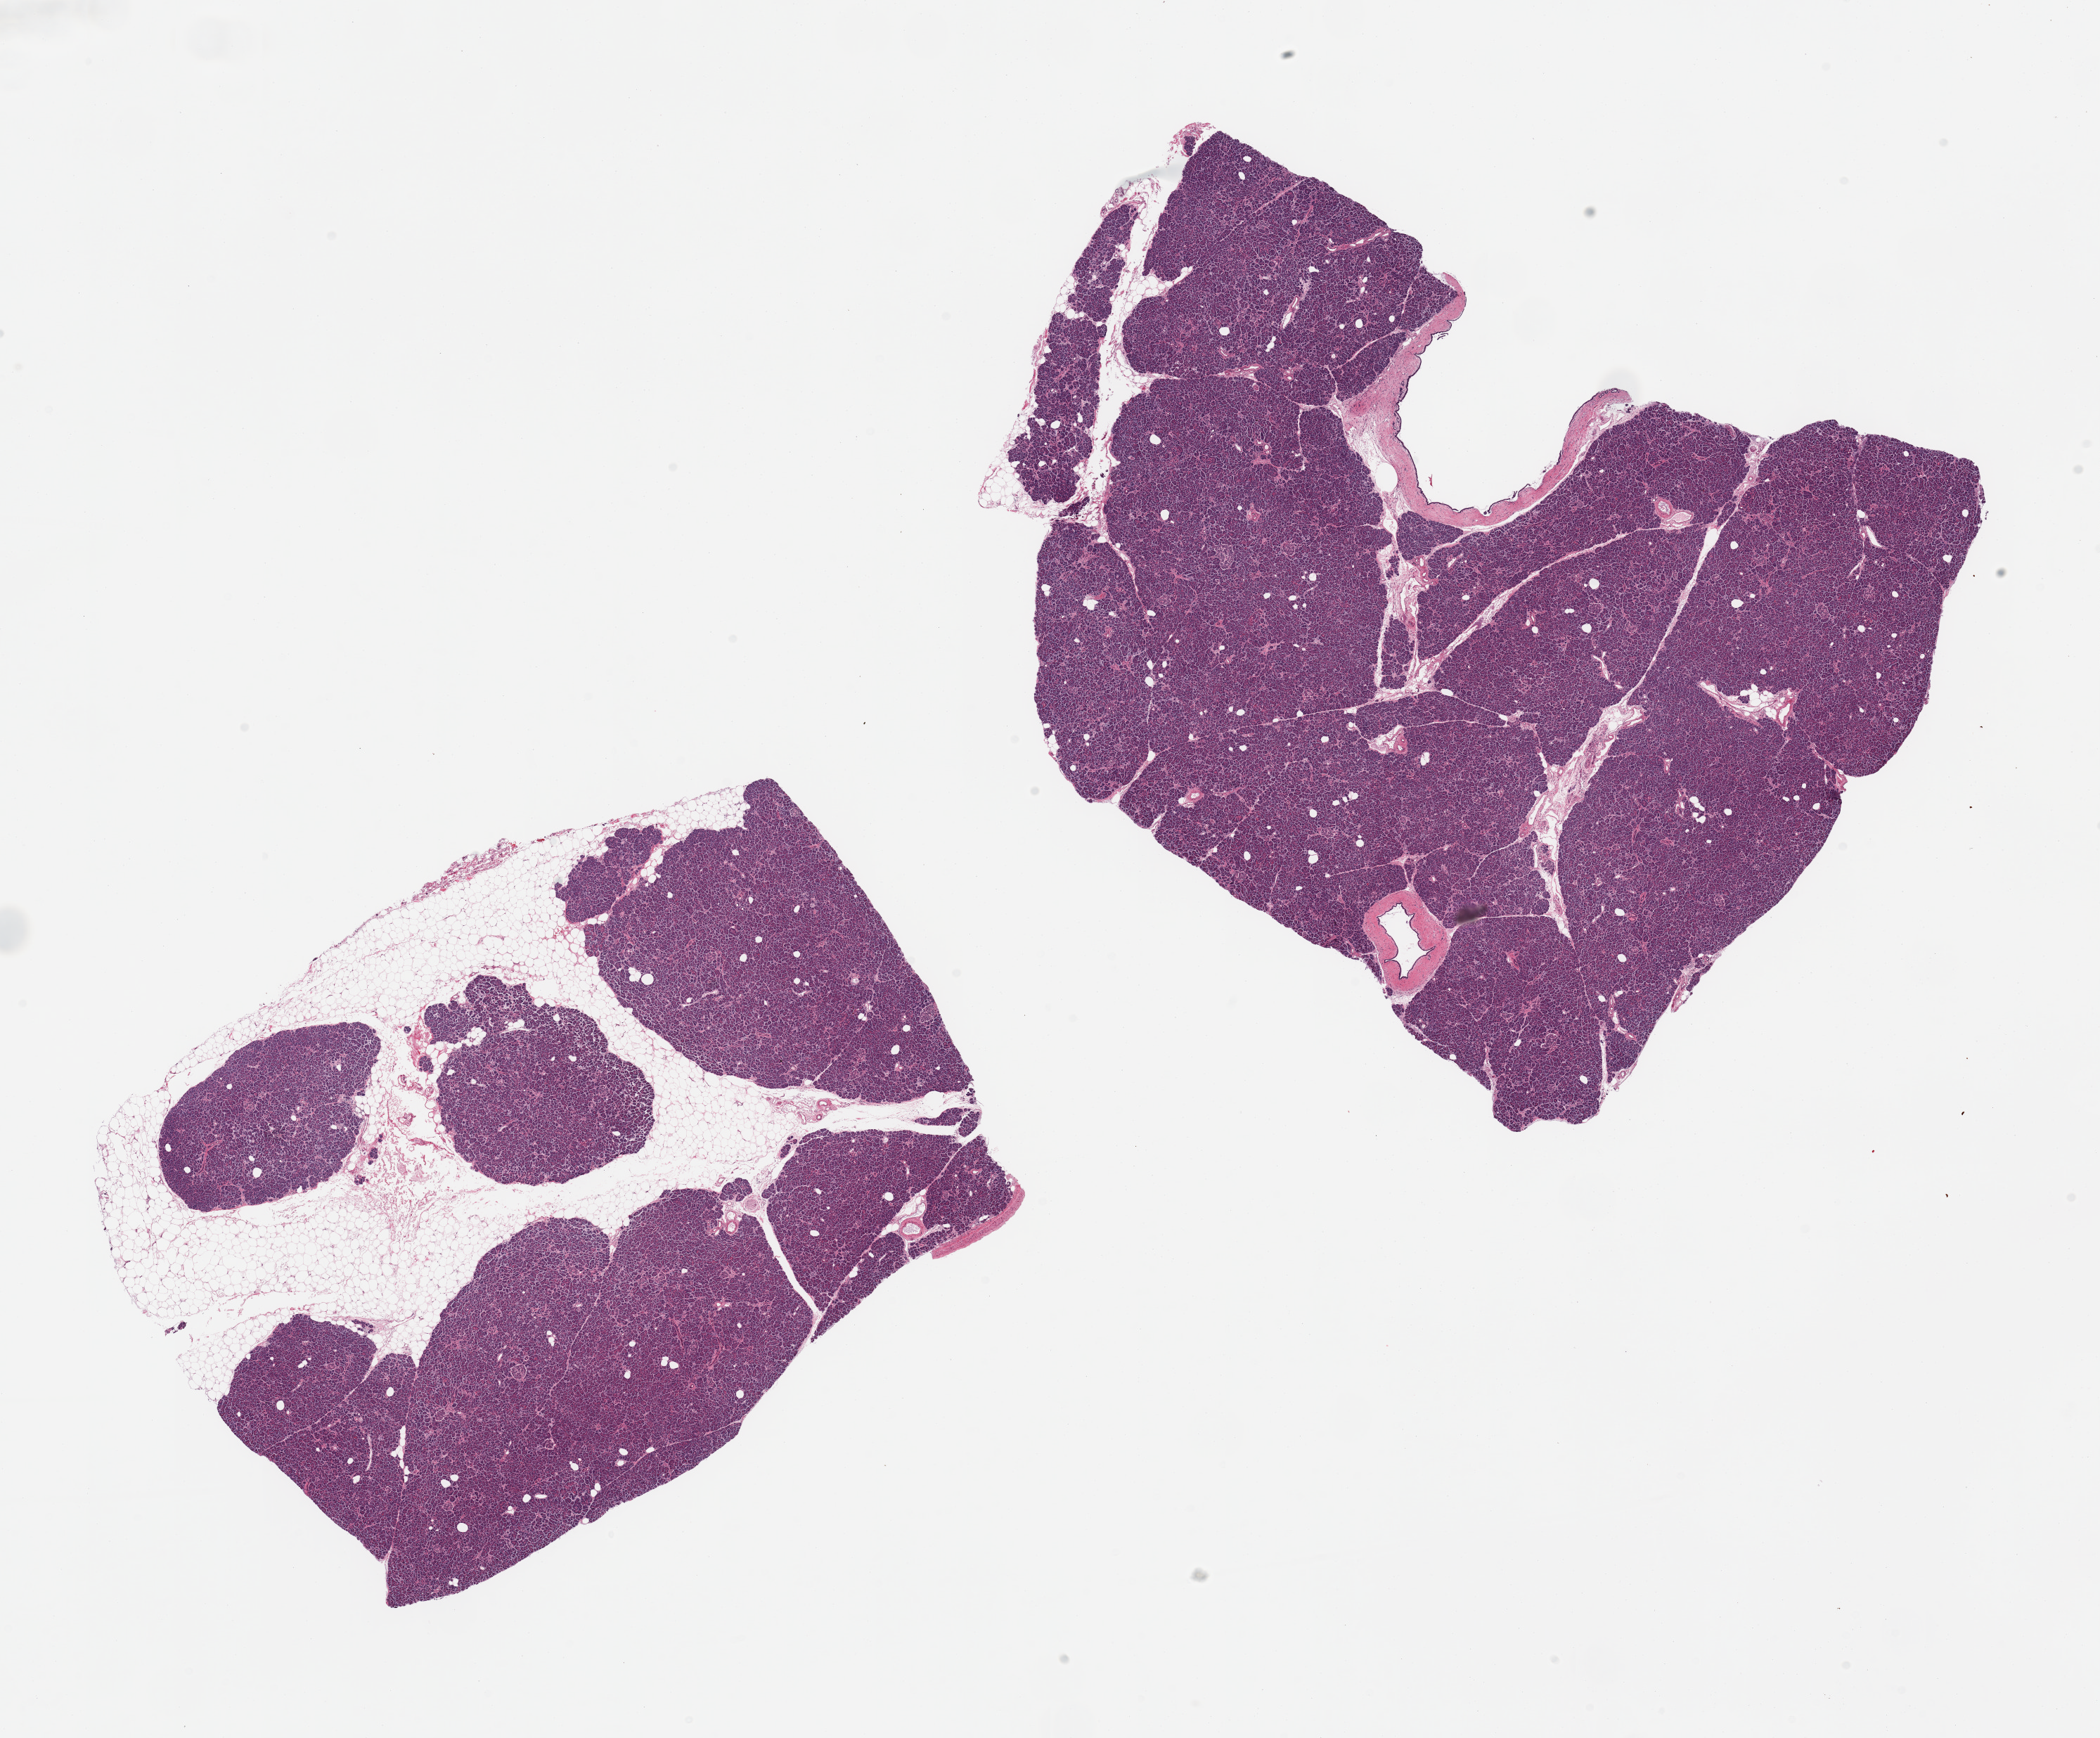
Digitized hematoxylin and eosin (H&E)-stained section — whole scanned area (about 23.6 x 19.6 mm, from a 20x scan) shown as a low-resolution overview, PAXgene-fixed paraffin-embedded (PFPE) section, target tissue: pancreas, donor tissue sample. Donor: female.
- review note (as recorded): 2 pieces; 40% internal fat in 1 piece